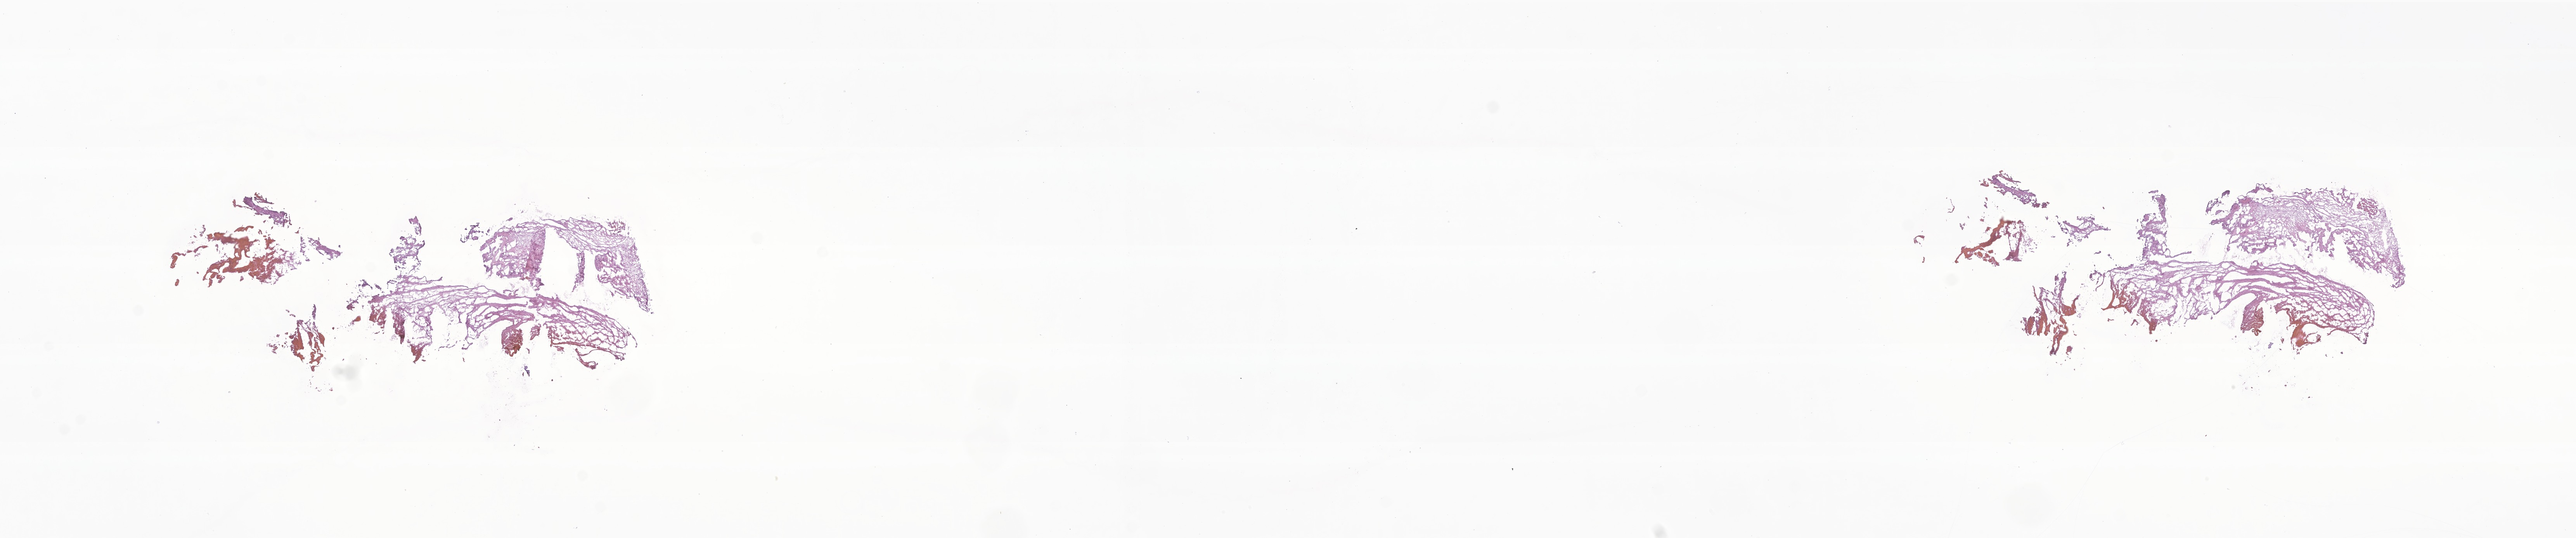
Digitized H&E-stained section of tumor tissue from the brain, shown as a low-resolution overview of the whole scanned area (about 28.0 x 5.8 mm), cryosection (OCT / tissue freezing medium). Patient: male, age 156 months (13 years).
Diagnosis: Neoplasm, malignant.